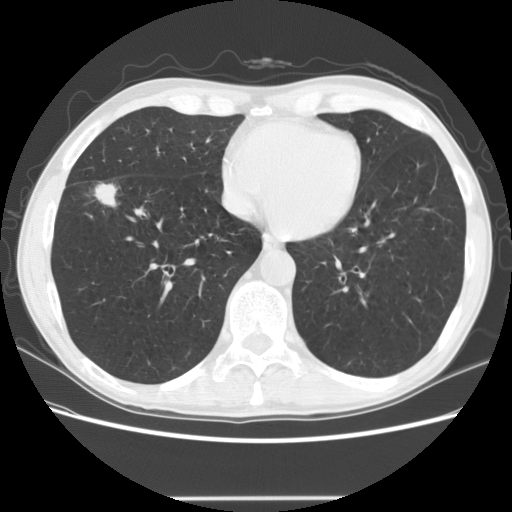
Axial slice from a low-dose chest CT screening exam, baseline annual screen, lung window (W 1500 / L -600 HU), 2.5 mm slice thickness, 140 kVp, 512 × 512 image matrix. Male participant, aged 69 years at enrolment. Current smoker at enrolment.
- Lesion marked by an expert reader, bounding box [x1, y1, x2, y2] px = [72, 166, 130, 218].
- Screening reader's record for this exam (one nodule recorded; not confirmed to be the boxed lesion): non-calcified nodule or mass ≥4 mm, right middle lobe, 20 × 14 mm, spiculated (stellate) margins, mixed attenuation.
- Official screen result: positive, change unspecified: nodule(s) >= 4 mm or enlarging nodule(s), mass(es), or other non-specific abnormalities suspicious for lung cancer.
- Lung cancer was diagnosed 86 days after this screen: squamous cell carcinoma, NOS, right middle lobe, poorly differentiated (G3), stage IA (AJCC 6th edition), 15 mm at pathology.